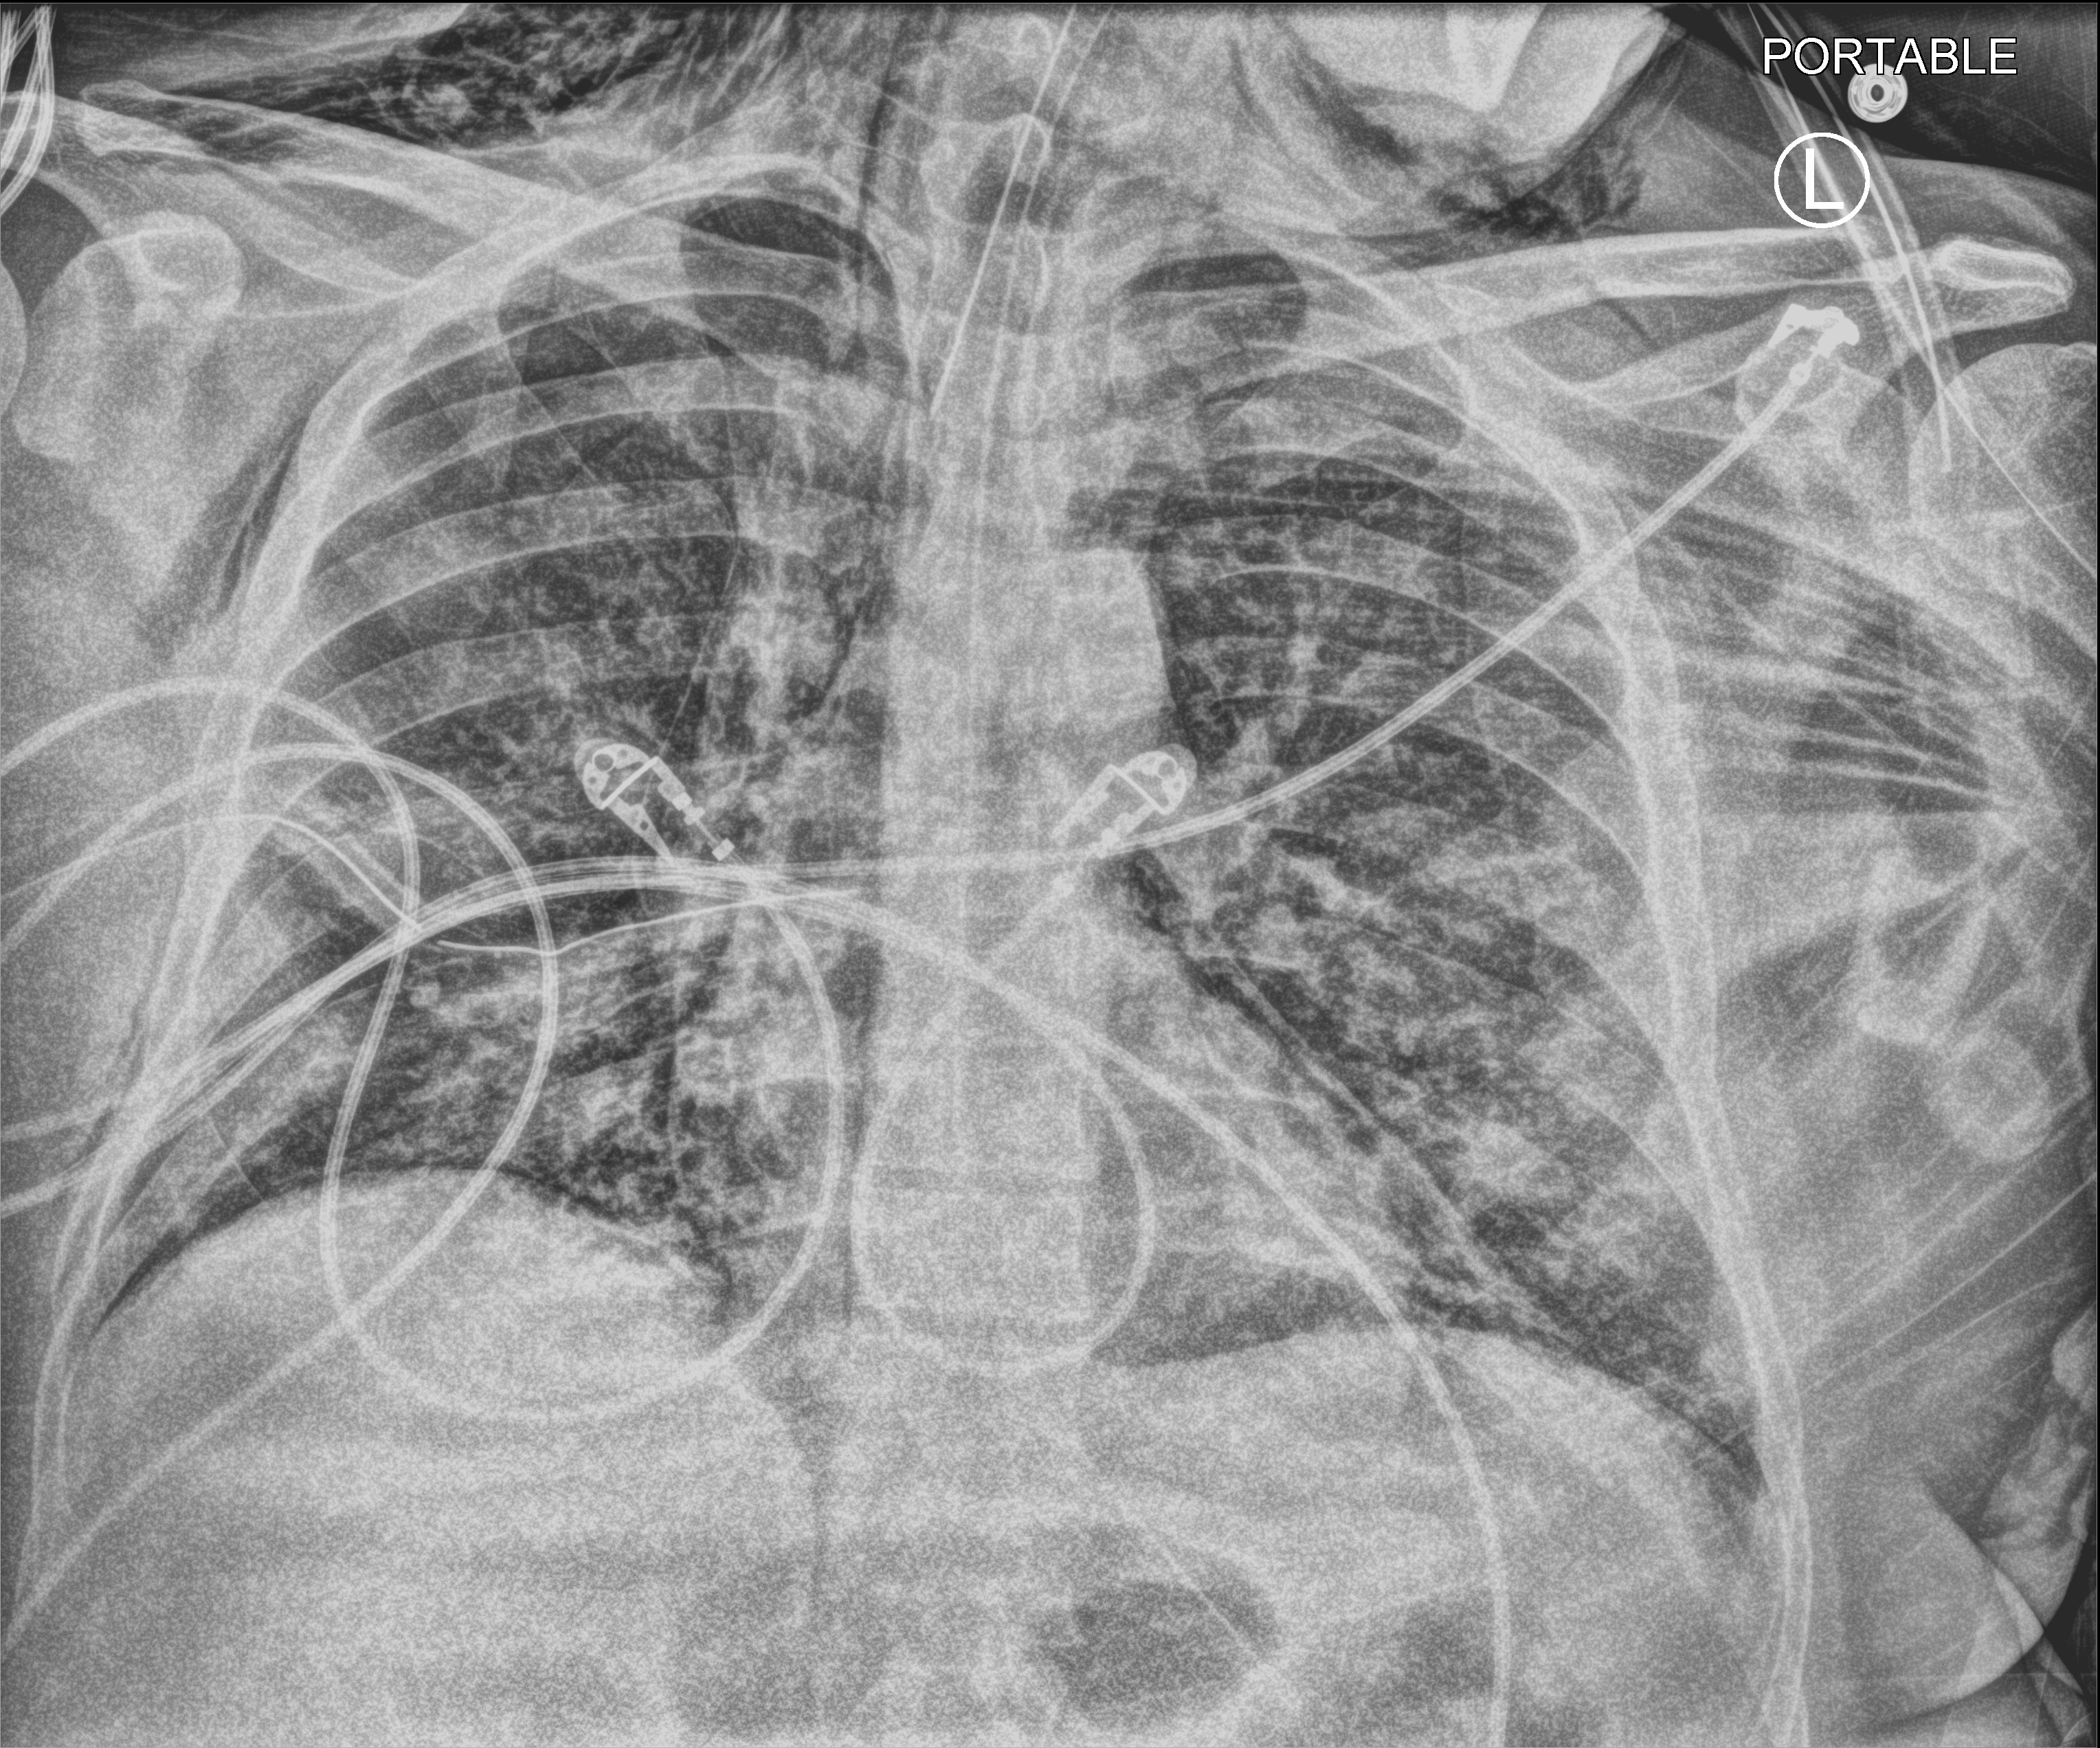
Chest X-ray (portable), anteroposterior (AP) projection. Male patient hospitalised with COVID-19, age 18–59 years.
From the hospital-stay record, not from the radiograph (when in the stay this image was taken is not recorded): hypertension (admission record): yes; other chronic lung disease (admission record): no.